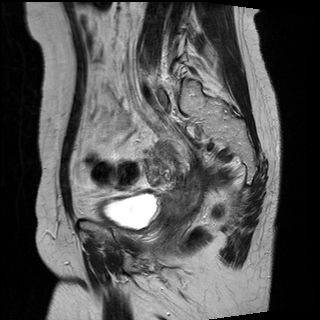
Pelvic MRI for cervical cancer, one sagittal slice. Position 8 of 27 along the scan axis. T2-weighted. 1.5 T. TE 89 ms, TR 2740 ms. 320 × 320 image matrix, field of view 260 × 260 mm. Patient: female, 42 years.
Annotated regions visible in this slice (manually delineated by an expert):
- uterus and cervix: bounding box [x1, y1, x2, y2] px = [161, 177, 202, 218]